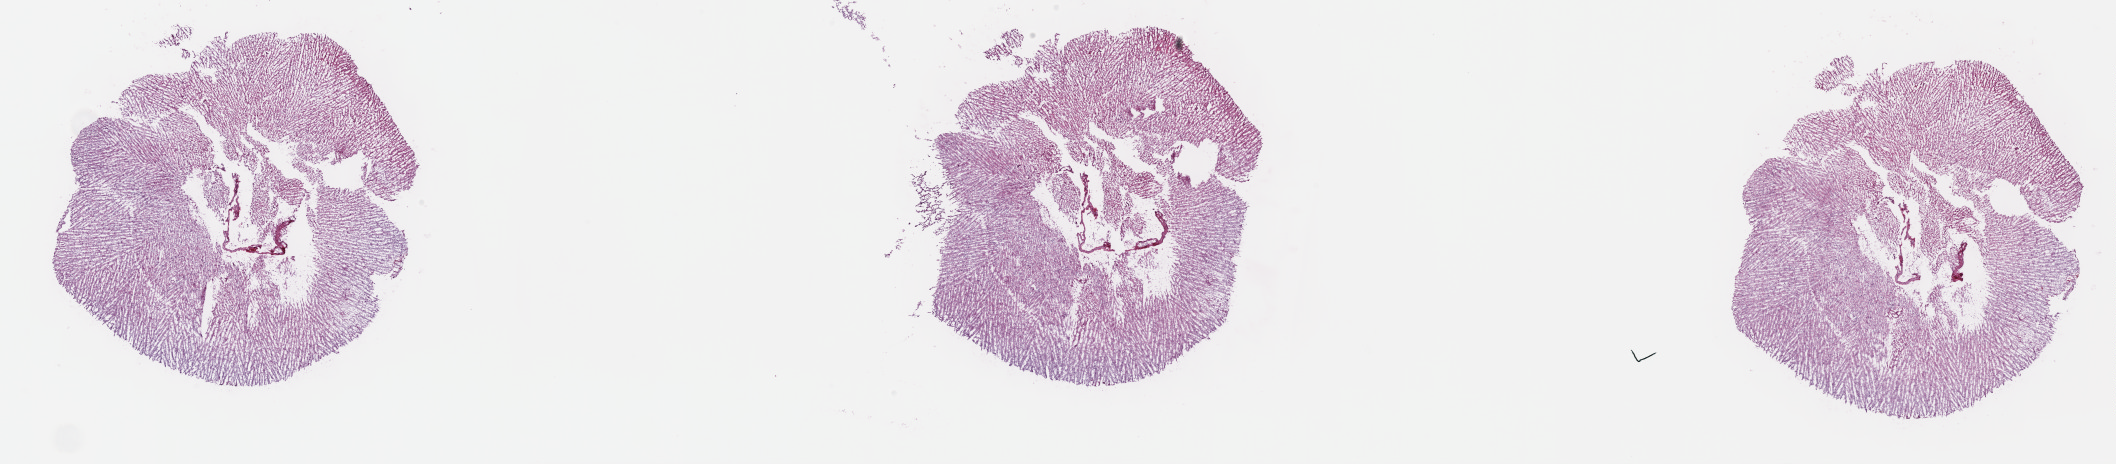
H&E whole-slide image, low-resolution overview of the scanned area, about 34.2 x 7.5 mm, frozen section, brain, primary tumour sample. Male, age 30 years at initial diagnosis. Histologic grade: G3 (poorly differentiated). Slide review estimates, as recorded: tumour cells 40%, tumour nuclei 90%, normal cells 10%, stromal cells 50%, necrosis 0%. Inflammatory infiltration, as recorded: lymphocyte infiltration 0%, monocyte infiltration 0%, neutrophil infiltration 0%.
Diagnosis: Astrocytoma, anaplastic (cerebrum).